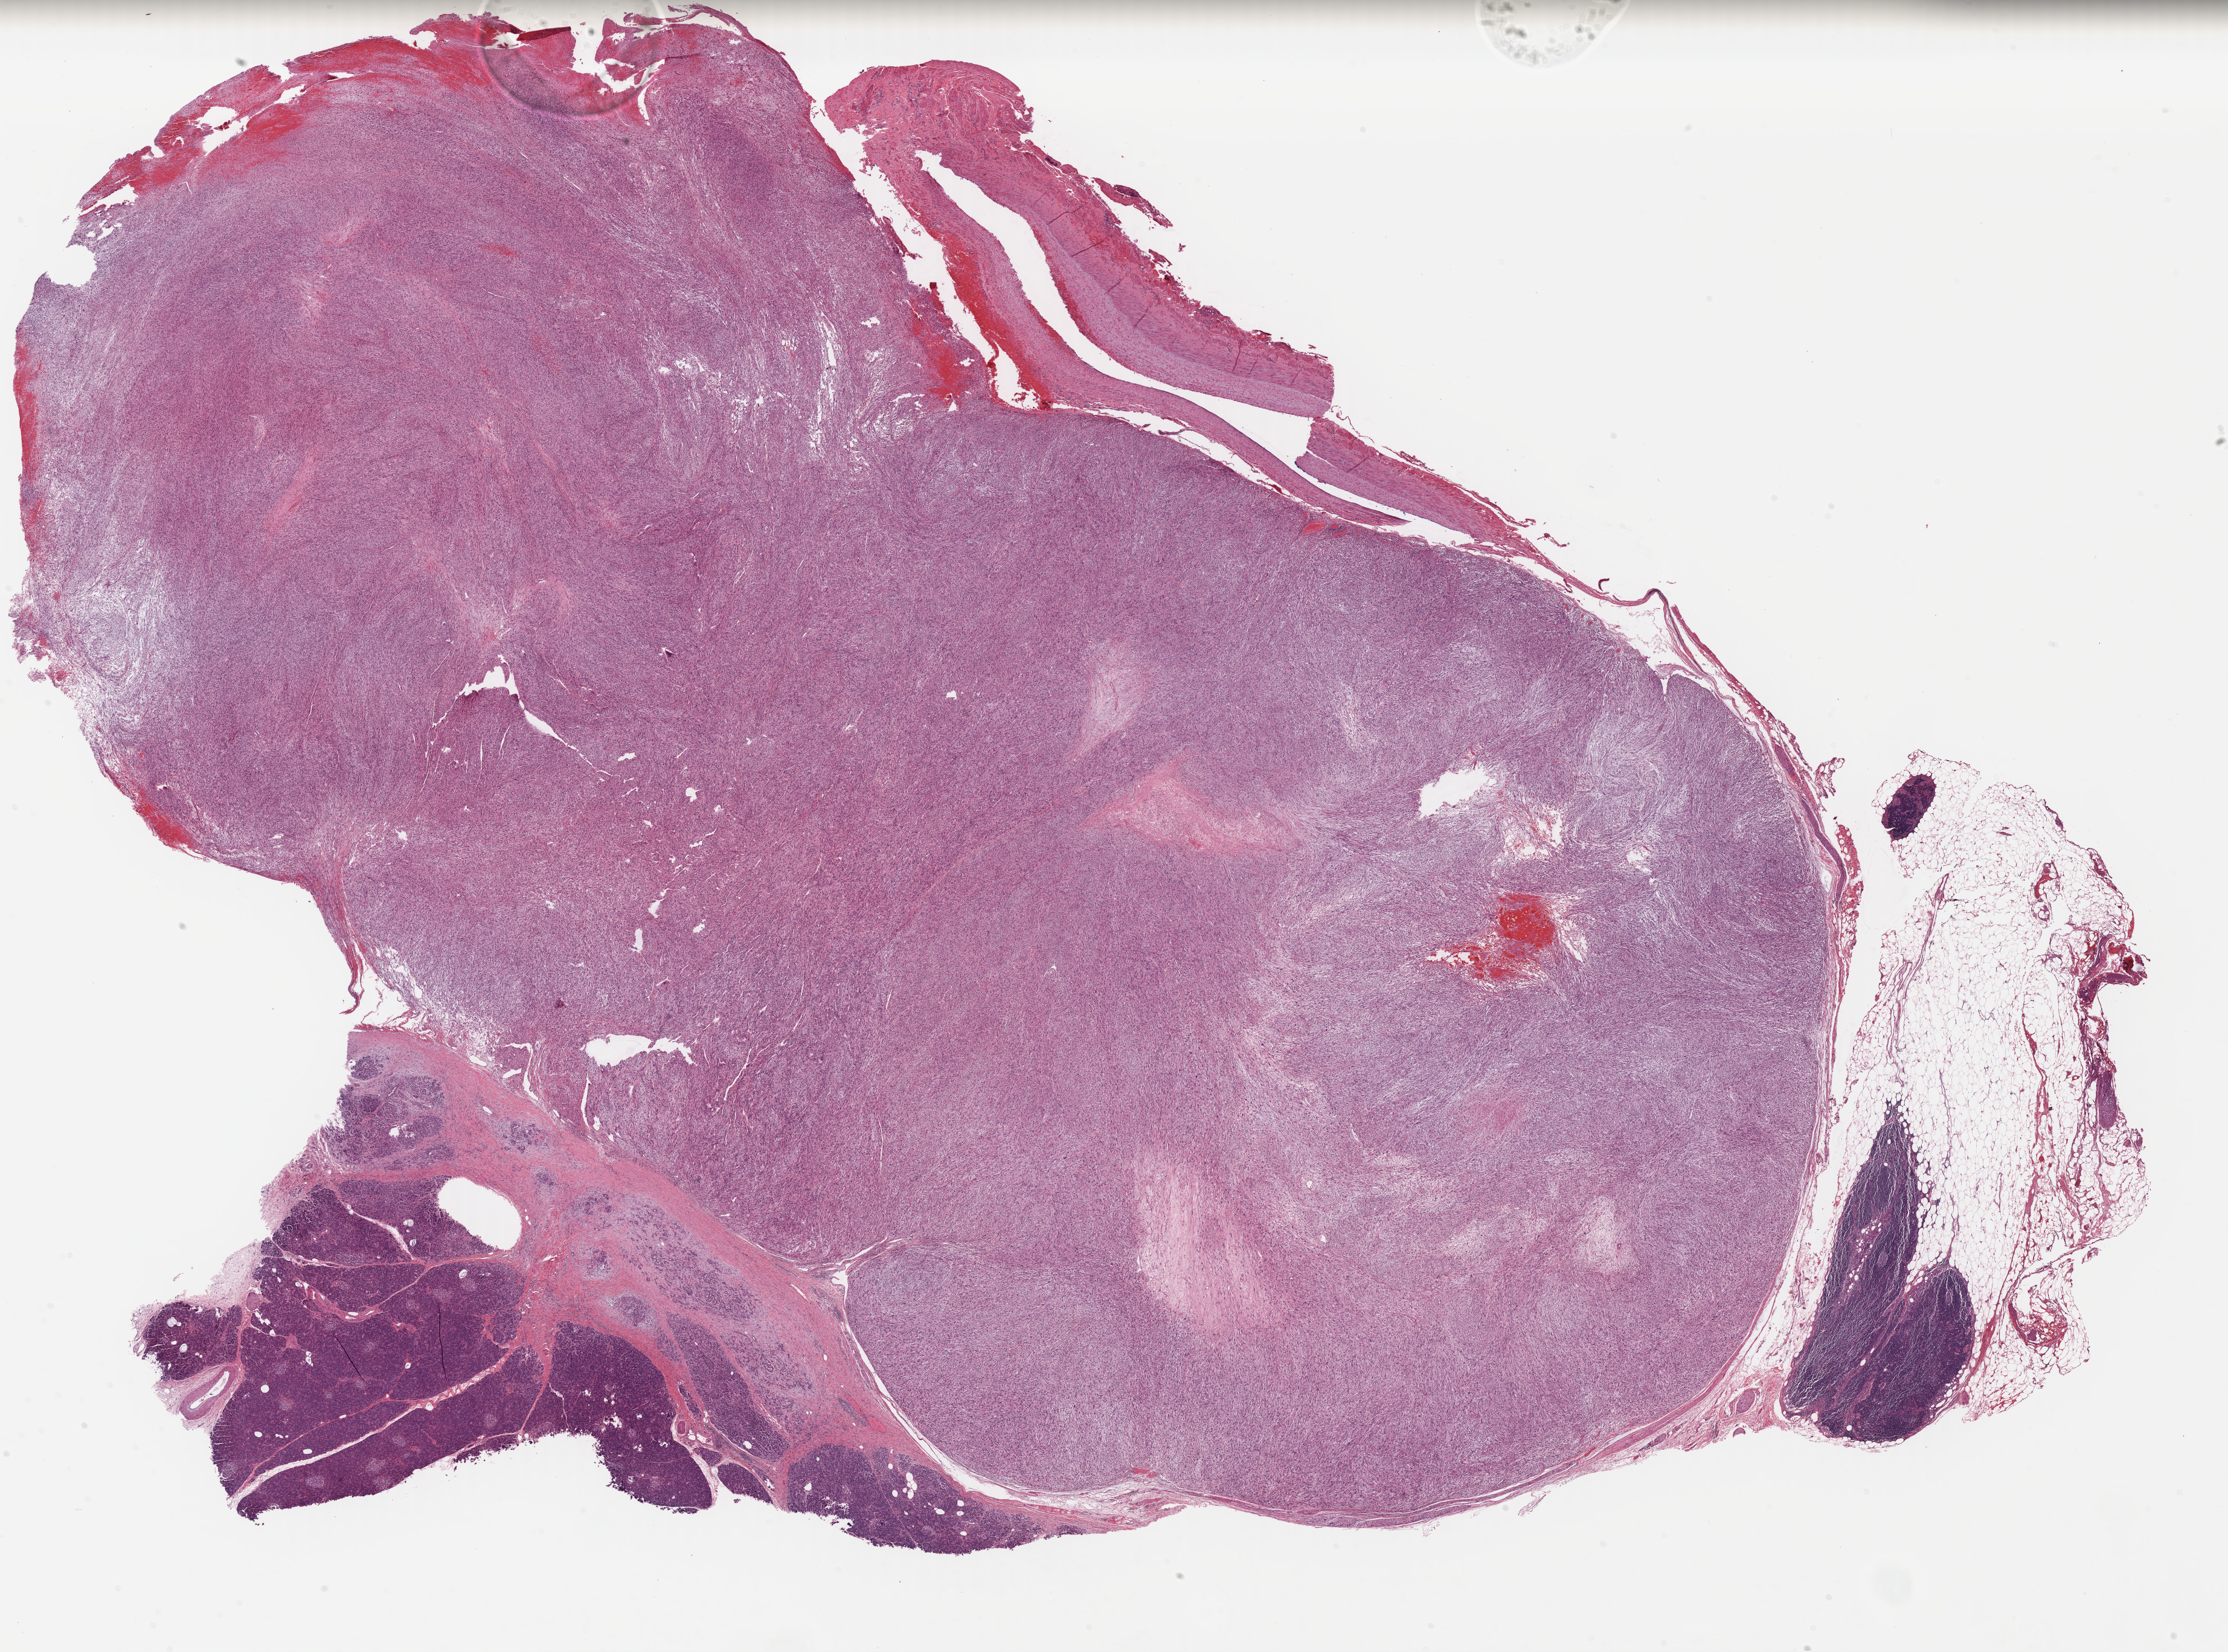
Hematoxylin and eosin (H&E) stained whole-slide image — low-resolution overview of the scanned area, about 29.0 x 21.5 mm (from a 40x scan); formalin-fixed paraffin-embedded (FFPE) diagnostic section; sample: primary tumour, retroperitoneum and peritoneum. Patient: female, age at initial diagnosis 65 years.
Diagnosis: Leiomyosarcoma, NOS (retroperitoneum).